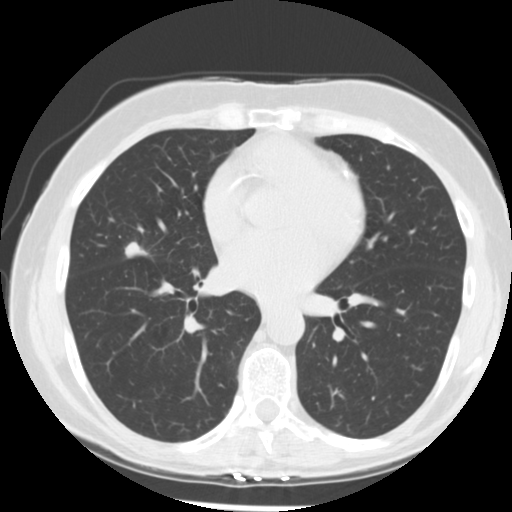
Axial slice from a low-dose chest CT screening exam; baseline screening round; lung window (W 1500 / L -600 HU); standard (soft-tissue) reconstruction kernel (STANDARD); slice 127 of 255 in the series; 512 × 512 image matrix, field of view 320 × 320 mm. Female participant, aged 66 years at enrolment. Former smoker at enrolment.
Expert-annotated lung lesion, bounding box (x1, y1, x2, y2) in pixels: (117, 230, 167, 267). The exam's reader record, not a measurement of the box and not confirmed to be the same lesion: non-calcified nodule or mass ≥4 mm, right middle lobe, 15 × 13 mm, poorly defined margins, soft tissue attenuation. Participant outcome: lung cancer diagnosed 27 days after this screen — adenocarcinoma, NOS, right middle lobe, undifferentiated (G4), stage IIIA (AJCC 6th edition), 18 mm at pathology.